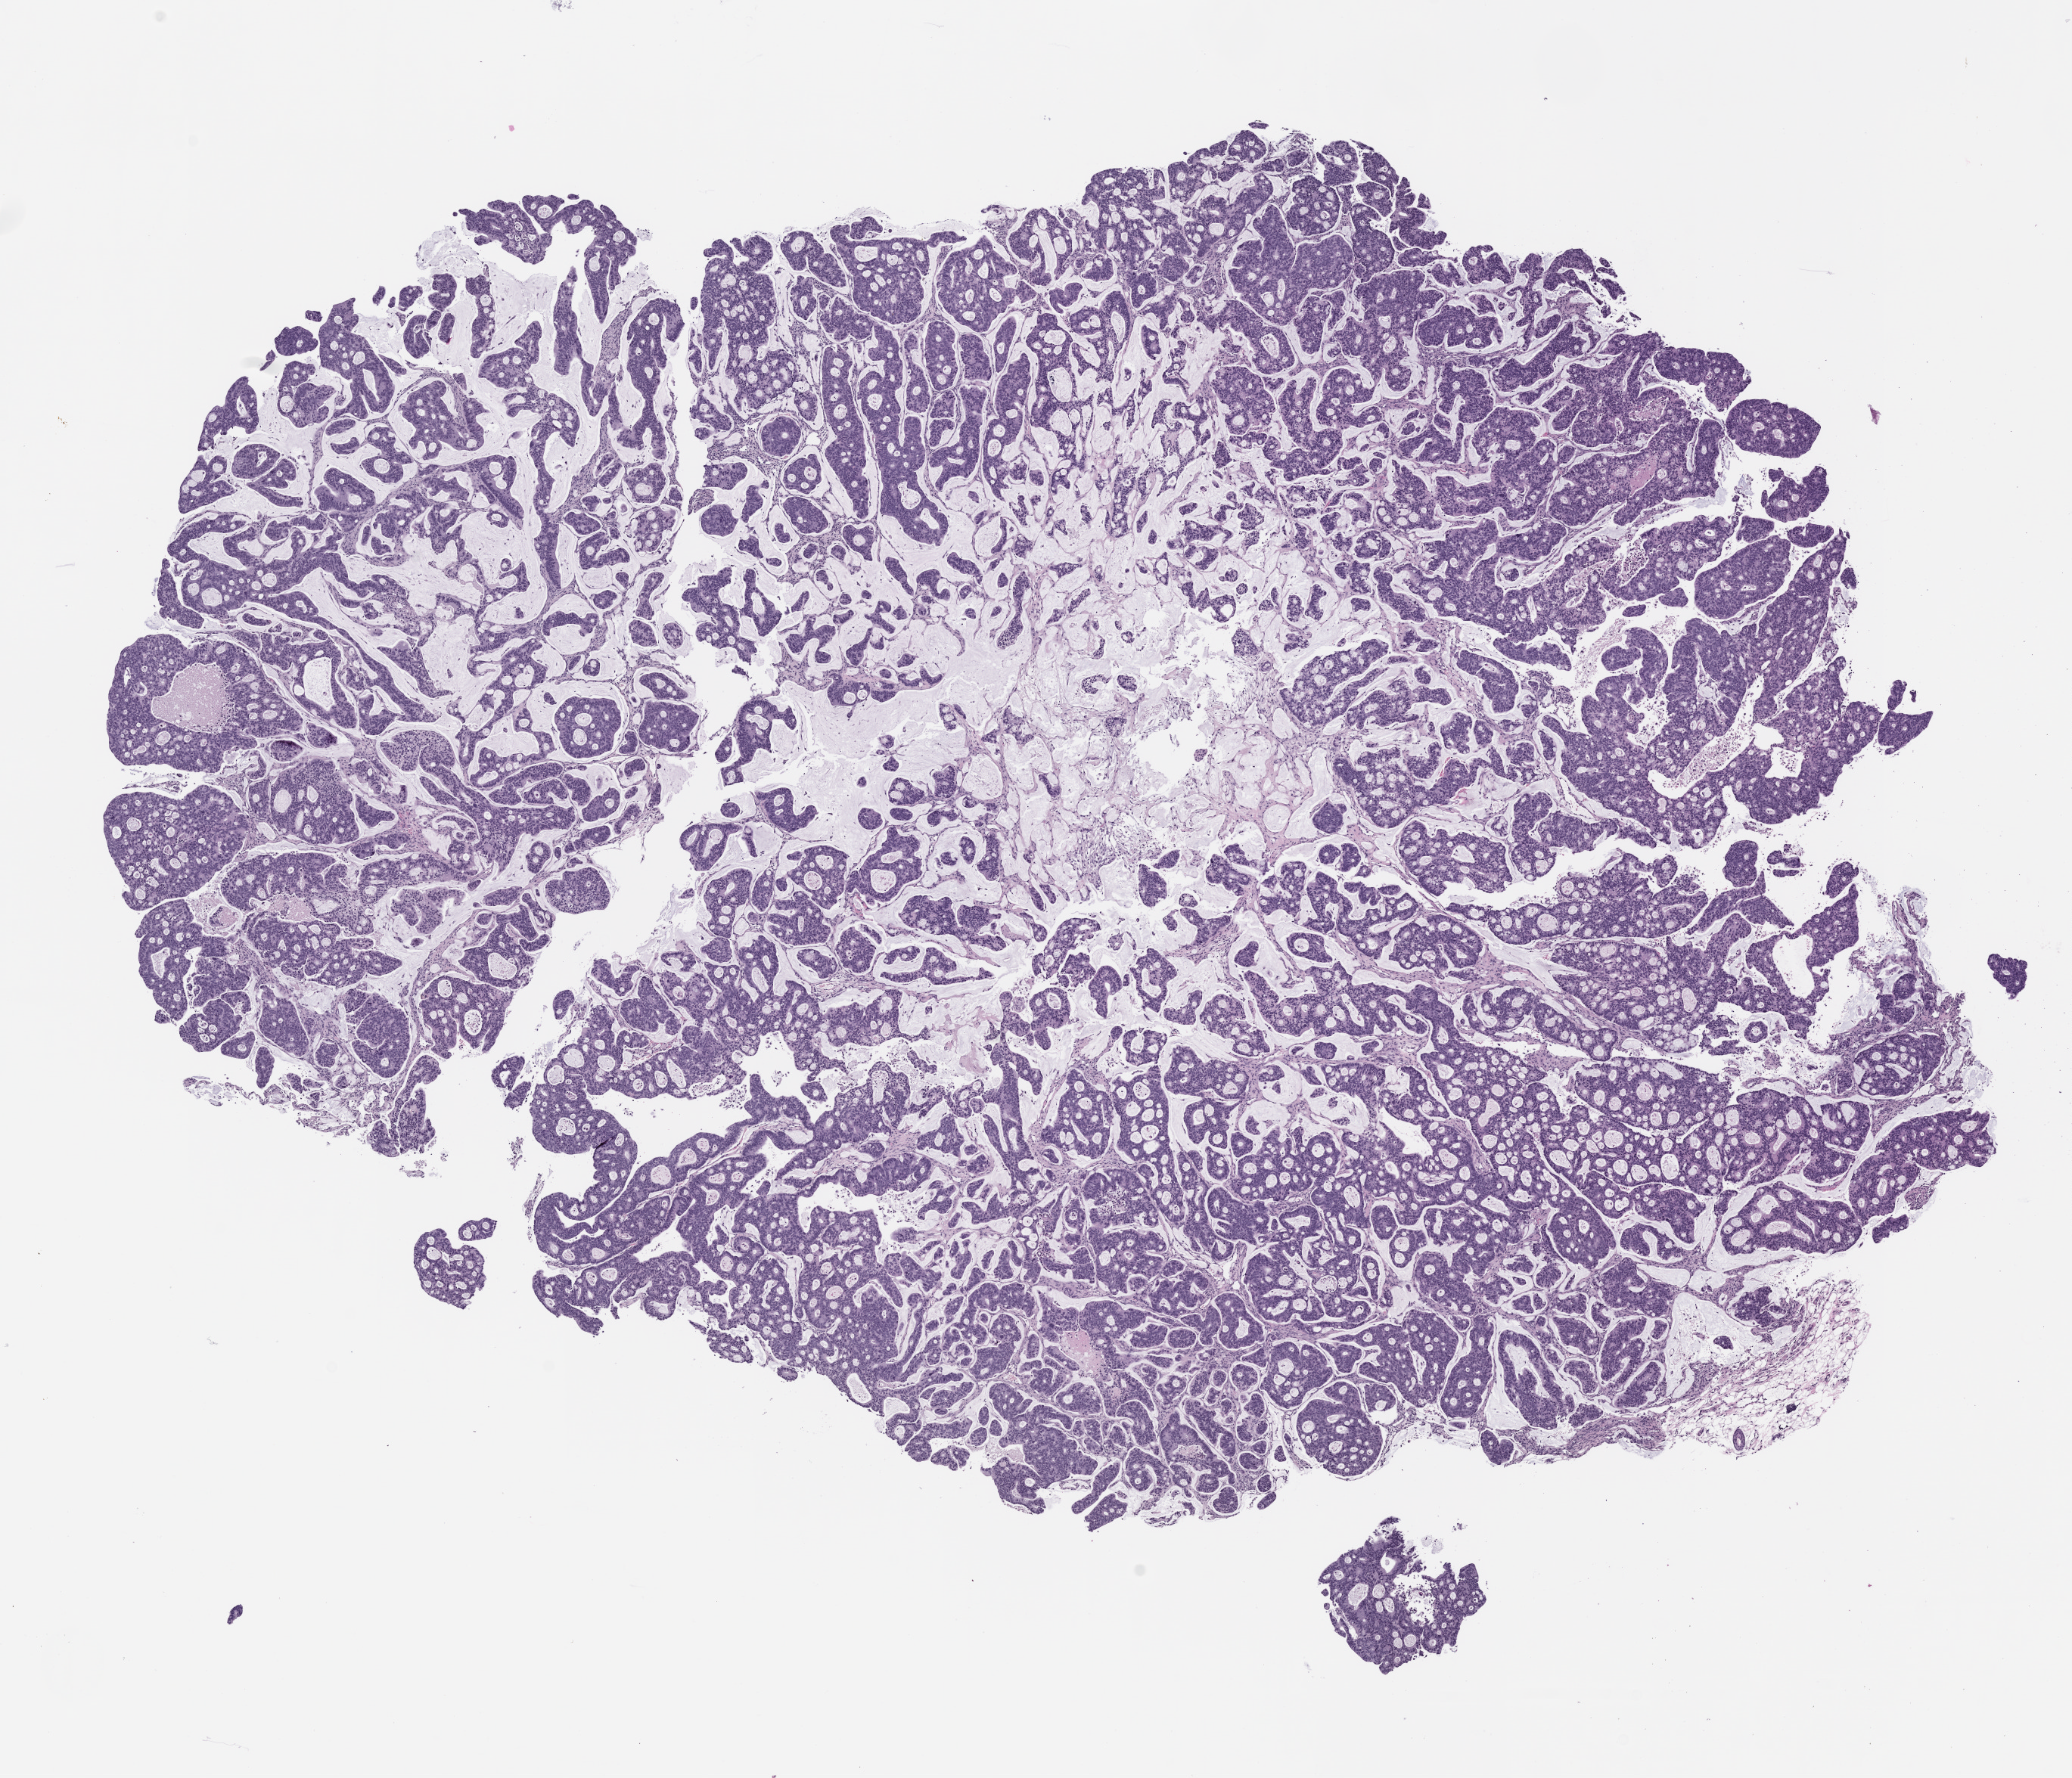
Whole-slide image, haematoxylin and eosin: patient-derived xenograft (human tumor grown in a mouse), passage 0 — low-resolution overview of the scanned area, about 11.0 x 9.5 mm, formalin-fixed paraffin-embedded section, tumor site category: colon.
- originating patient diagnosis: Colon Adenocarcinoma